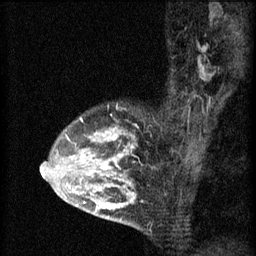
Breast MRI (dynamic contrast-enhanced), one sagittal slice; position 44 of 60 along the scan axis; 3 images stored at this slice position (order not interpretable as contrast timing); 1.5 T; TE 4.2 ms, TR 8.2 ms; 256 × 256 image matrix, field of view 180 × 180 mm. Patient: female, 45 years.
Structures marked on this image (semi-automatic segmentation, software-assisted and operator-edited):
- analysis volume of interest (the breast-tissue region the enhancement analysis was run in; not a lesion): bounding box <54,106,137,217> (left, top, right, bottom; pixels)
- tumour enhancement mask (voxels above the 70 % enhancement threshold inside the analysis volume of interest): <54,118,137,211>